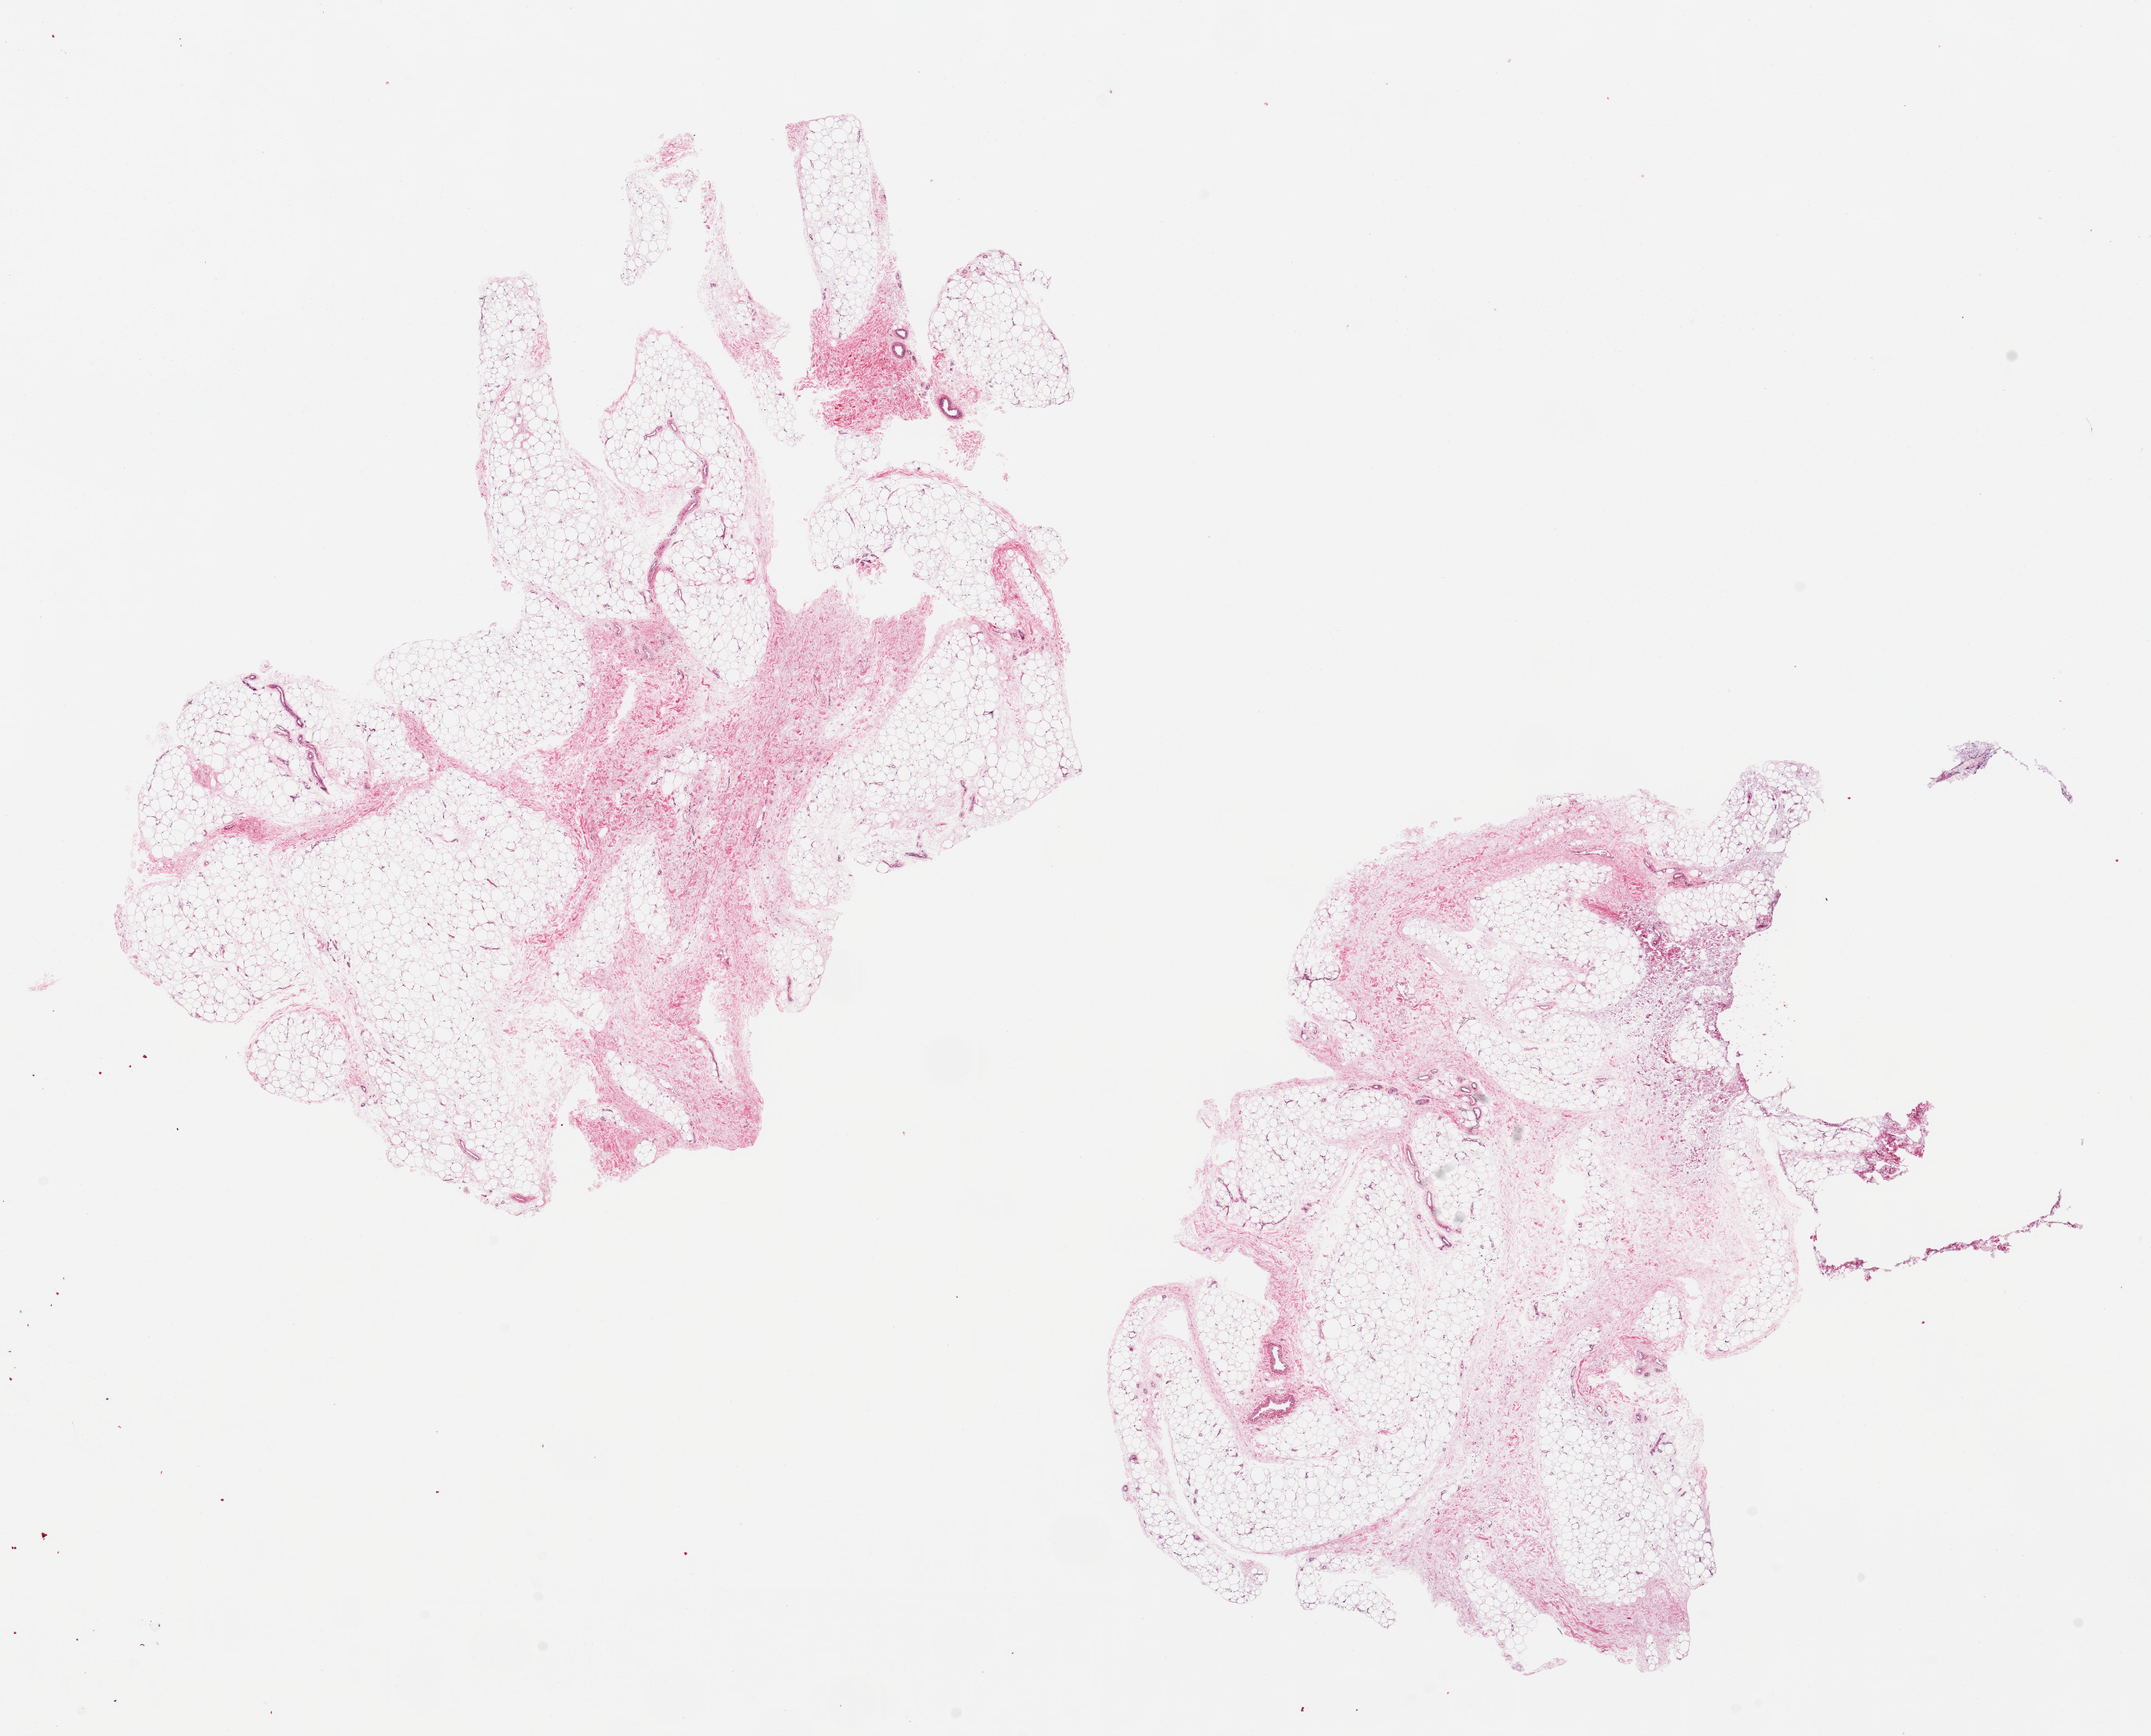
Digitized hematoxylin and eosin (H&E)-stained section, brightfield, whole scanned area (about 21.7 x 17.5 mm, from a 20x scan) shown as a low-resolution overview, PAXgene-fixed, paraffin-embedded tissue, target tissue: adipose tissue, tissue donor sample. Male donor.
Reviewer comment on this tissue sample: 2 ~ 10x5.5mm pieces, well-fixed.